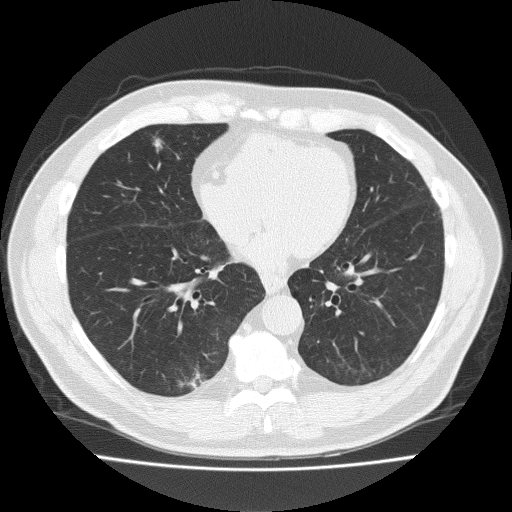
Low-dose screening chest CT, axial slice, second screening round (one year after baseline), lung window (W 1500 / L -600 HU), 2 mm slice thickness, slice 115 of 184 in the series, 512 × 512 image matrix. Male, age 57 years at enrolment. Current smoker at enrolment.
- Expert reader's lesion annotation, bounding box [x1, y1, x2, y2] px = [135, 130, 177, 169].
- Reader record for this screening exam (exam-level; its link to the box is not recorded): non-calcified nodule or mass ≥4 mm, right middle lobe, 8 × 7 mm, spiculated (stellate) margins, soft tissue attenuation, pre-existing on the prior screen: yes; interval growth: yes.
- Lung cancer was diagnosed 67 days after this screen: adenocarcinoma, NOS, right middle lobe, moderately differentiated (G2), stage IA (AJCC 6th edition), 12 mm at pathology.